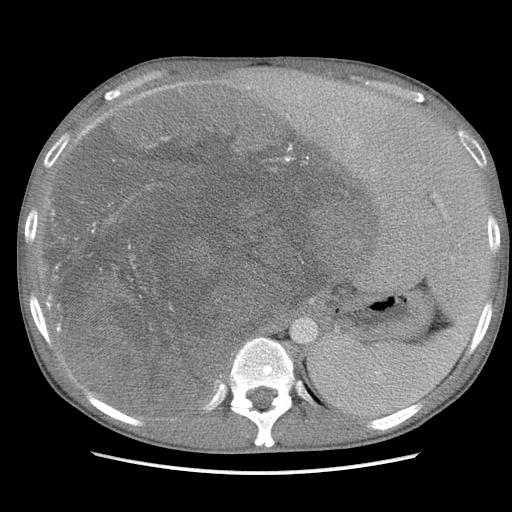
Contrast-enhanced abdominal CT, one axial slice. Slice 79 of 115 in the series (ordered by position). Soft-tissue window (W 400 / L 40 HU). 512 × 512 image matrix, field of view 360 × 360 mm. Male patient. Case-level facts recorded for this patient, not image findings: diagnosis: adrenocortical carcinoma; tumour side: right adrenal; Ki-67 index: 13 %; stage (as recorded): 3.
Outlined on this slice (semi-automatic segmentation, software-assisted and operator-edited):
- mass: bounding box [x1, y1, x2, y2] px = [49, 91, 365, 411]